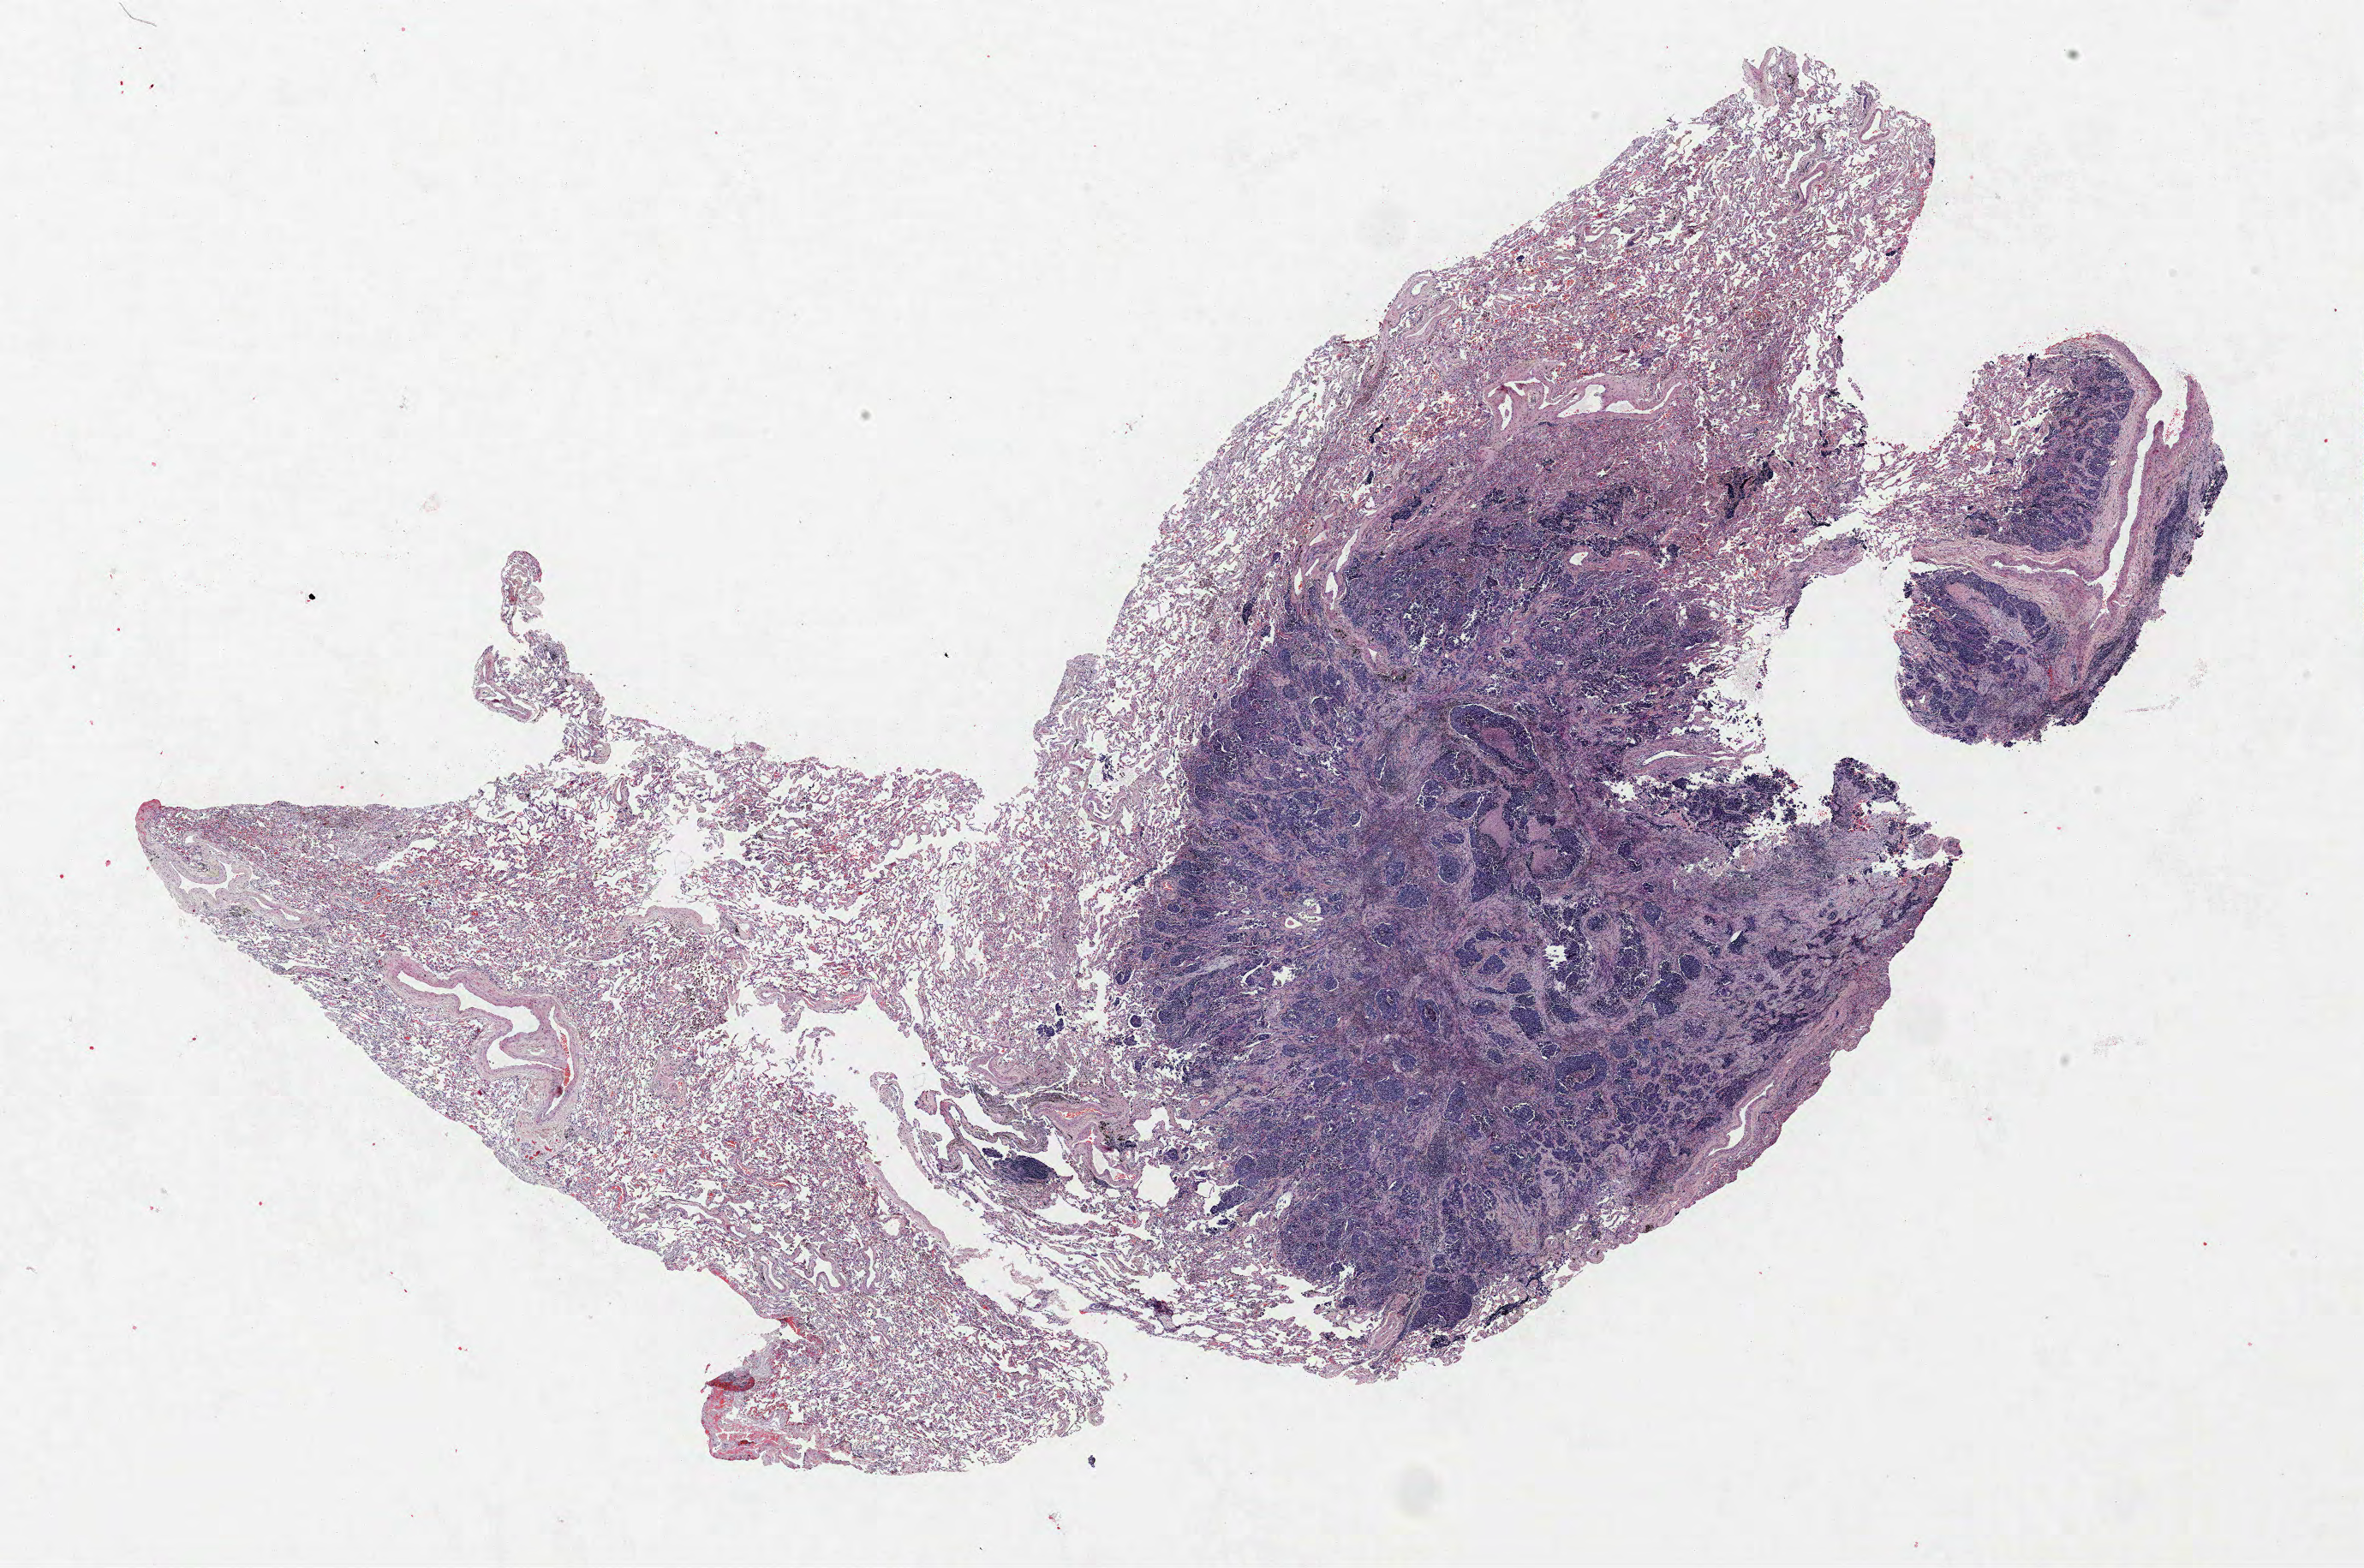
Whole-slide histology image, H&E — shown as a low-resolution overview of the whole scanned area (about 22.1 x 14.7 mm, from a 40x scan), FFPE section, lung tissue. Male patient, aged 55 at enrolment. Current smoker at enrolment.
Participant's lung-cancer diagnosis: Large cell neuroendocrine carcinoma.